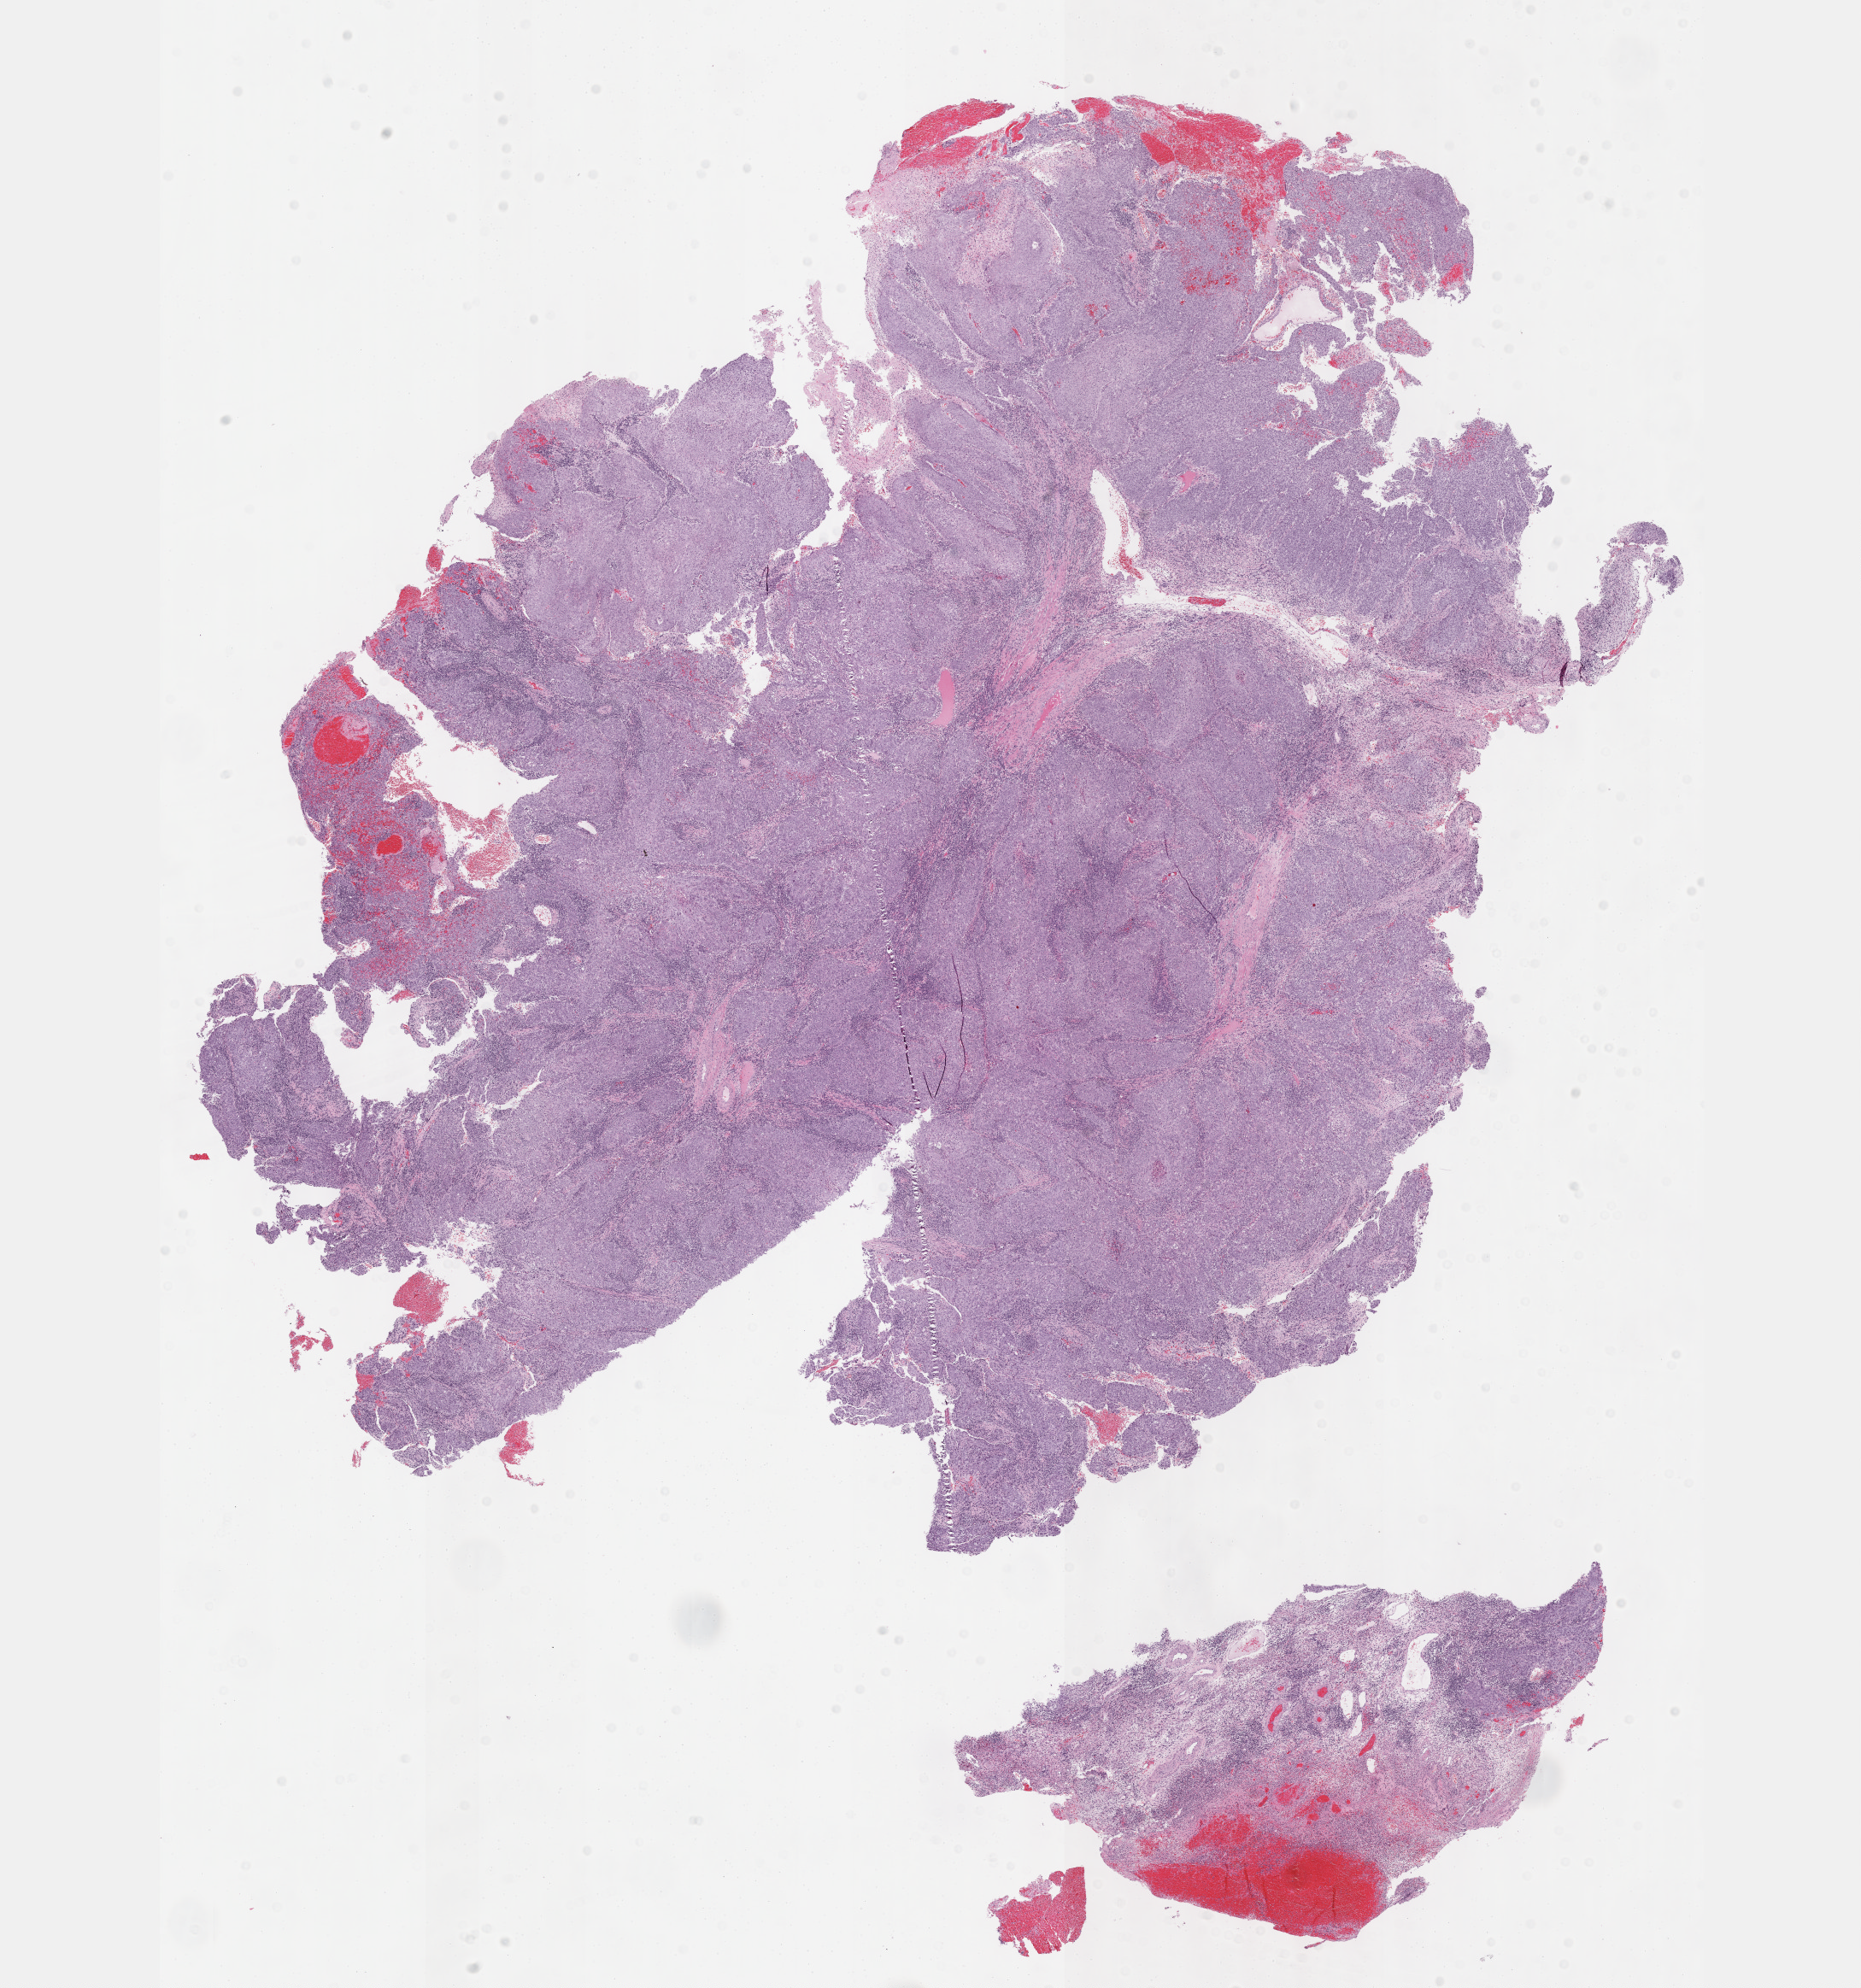
H&E-stained whole-slide image, shown as a low-resolution overview of the whole scanned area (about 17.6 x 18.8 mm, from a 40x scan), formalin-fixed paraffin-embedded (FFPE) diagnostic section, primary tumour sample from the cervix. Patient: female, age at initial diagnosis 37 years.
Pathologic diagnosis: Squamous cell carcinoma, large cell, nonkeratinizing, NOS (cervix uteri).